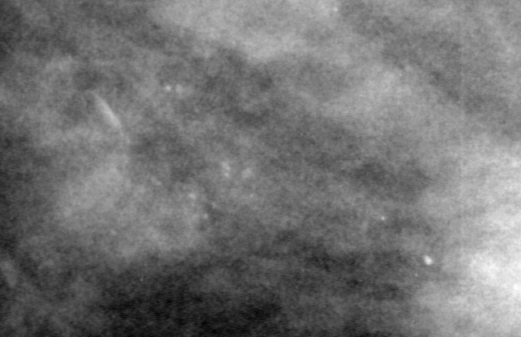
Region of interest cut from a scanned film mammogram (one marked finding), right breast, CC view.
- Marked abnormality: calcifications, morphology pleomorphic, distribution clustered; BI-RADS assessment category 4; pathology (as recorded): benign.